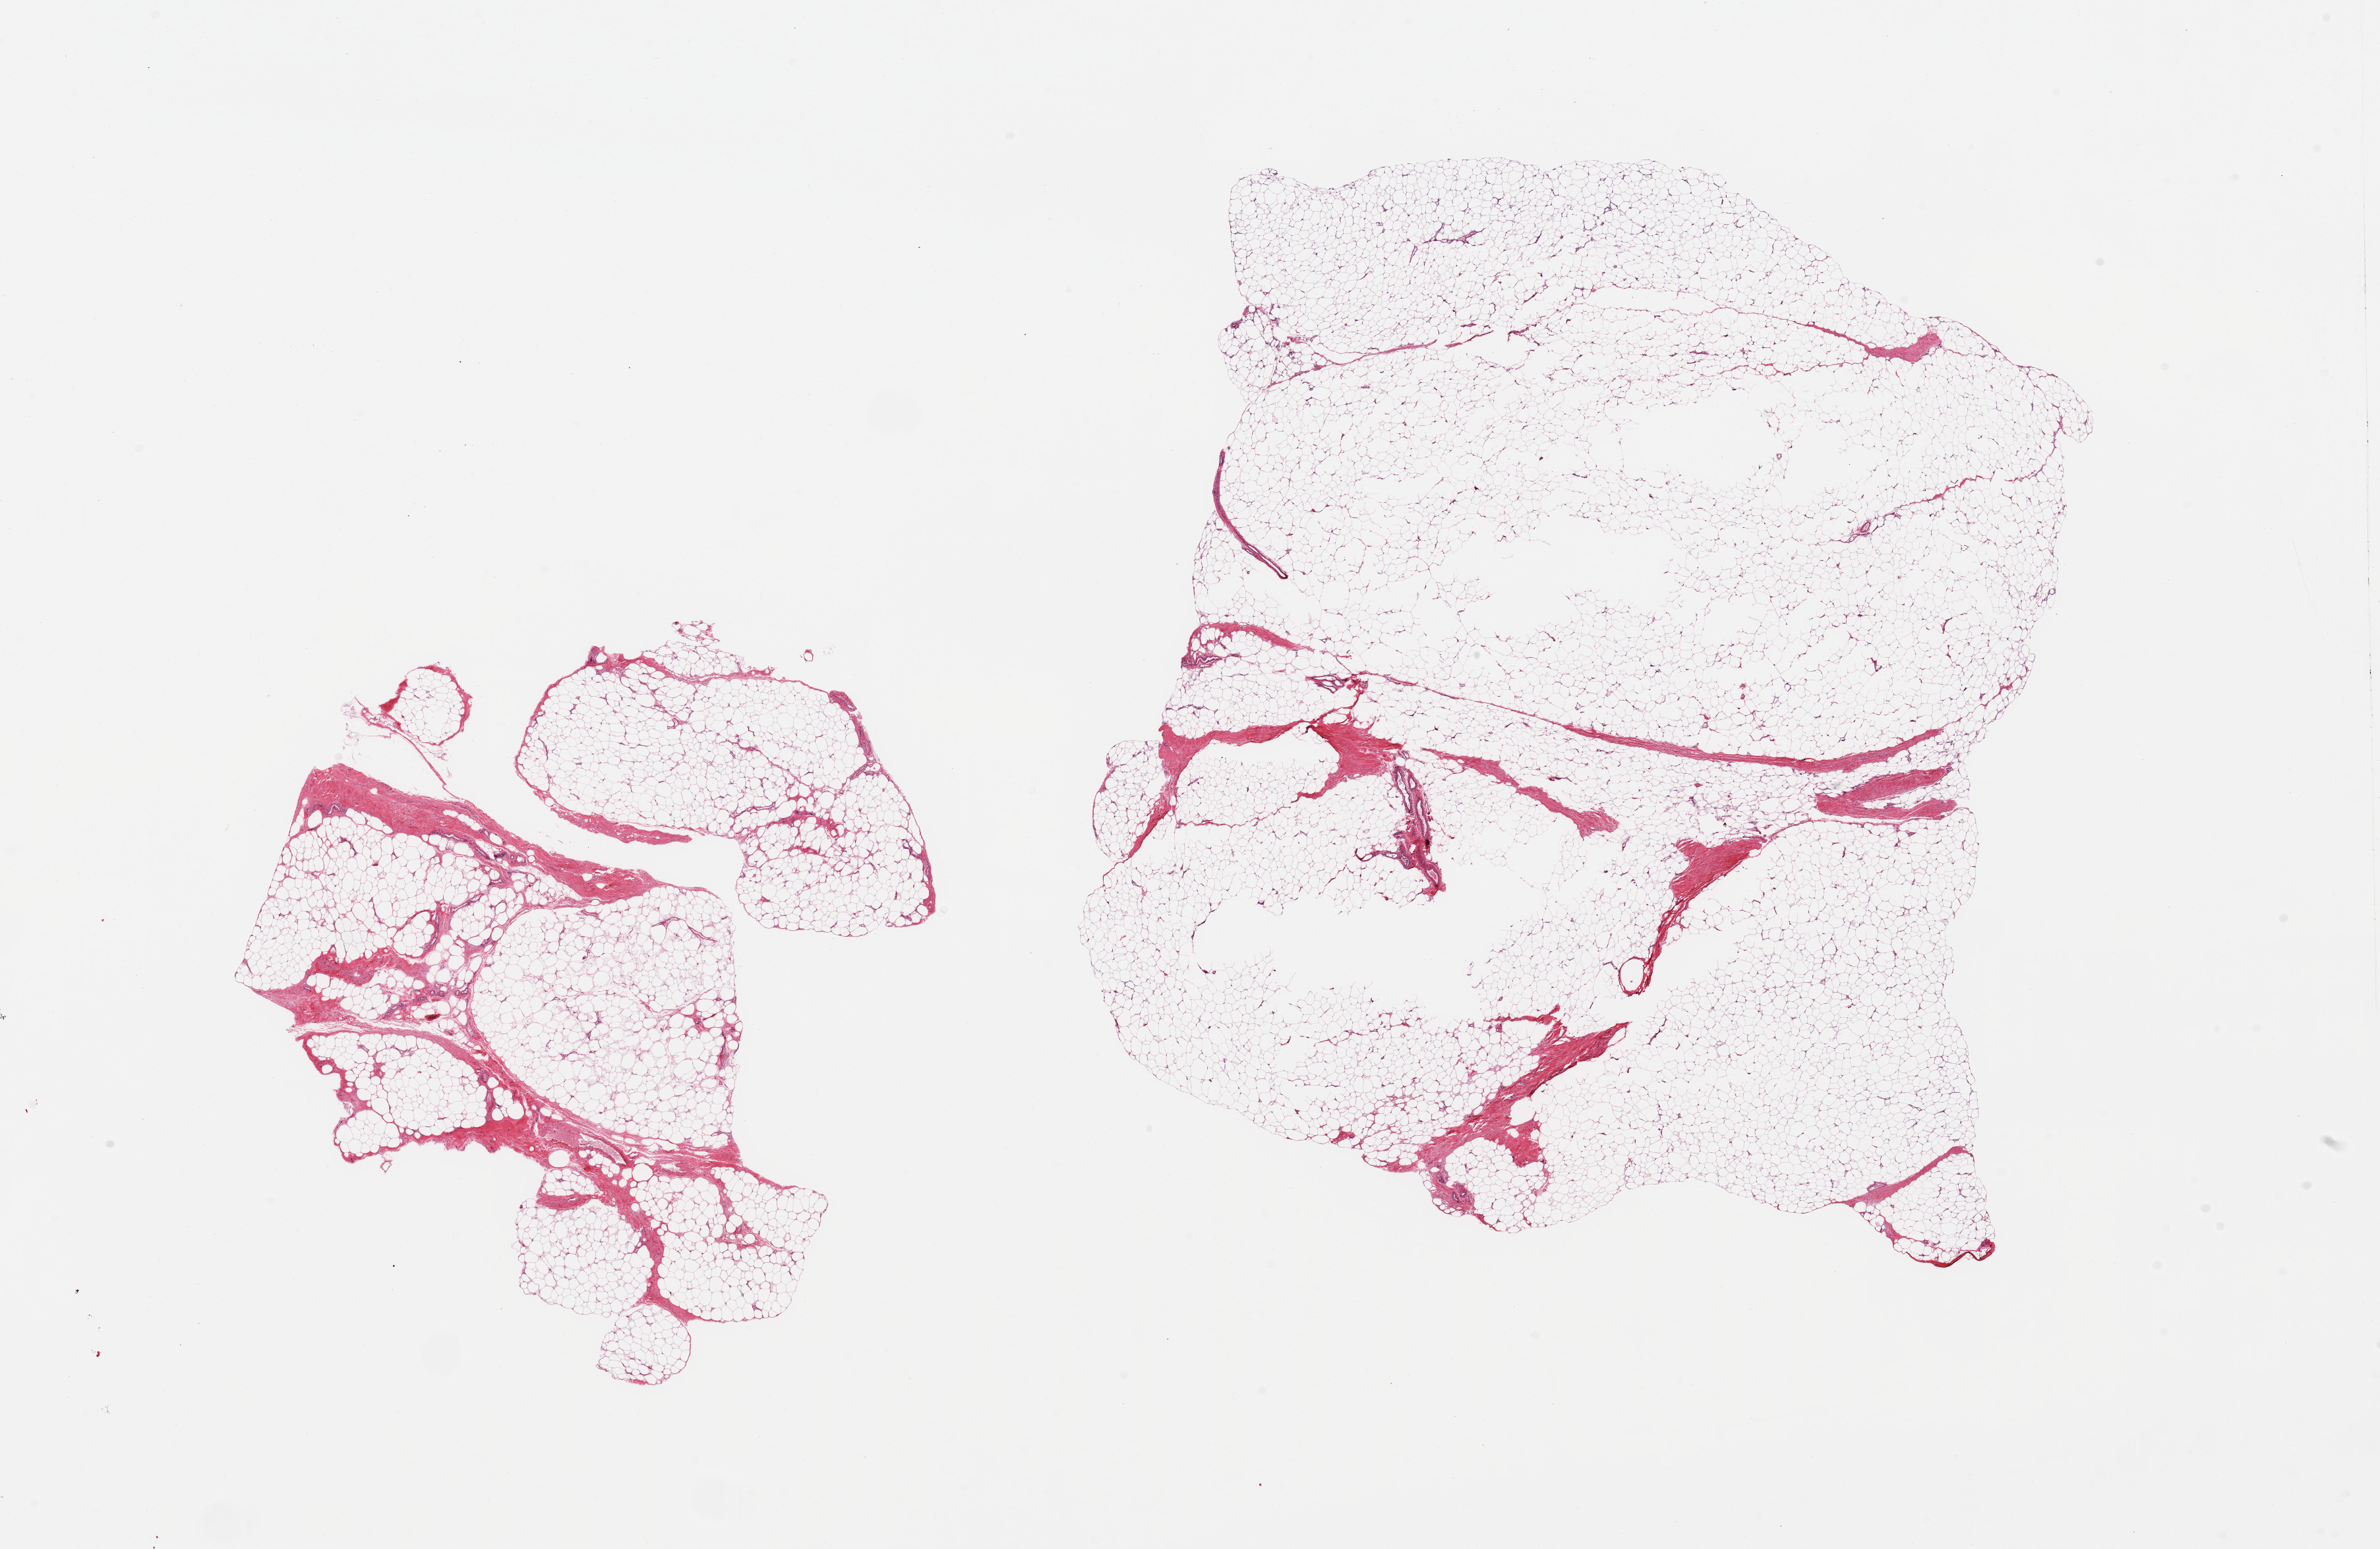
Whole-slide image, hematoxylin and eosin (H&E) stain, brightfield — shown as a low-resolution overview of the whole scanned area (about 28.5 x 18.6 mm, slide scanned at 20x), PAXgene-fixed, paraffin-embedded tissue, target tissue: adipose tissue, donor tissue sample. Donor sex: male.
- pathologist's review note for this sample: 2 pieces, ~10% fascia/vascular elments